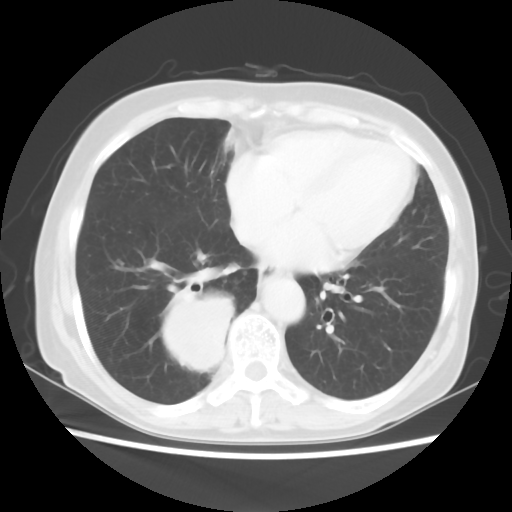
Chest CT, one axial slice; position 20 of 56 along the scan axis; reconstruction kernel STANDARD; 120 kVp; lung window (W 1500 / L -600 HU); 5 mm slice thickness; 512 × 512 image matrix. Patient: female, 66 years. From the clinical record (not read from this slice): clinical TNM (as recorded): T2 N3 M0; histopathological grade: G3.
Outlined on this slice (rectangle marked by the reading radiologist):
- lung tumour (recorded histology: small cell carcinoma): bounding box [x1, y1, x2, y2] px = [165, 284, 231, 382]